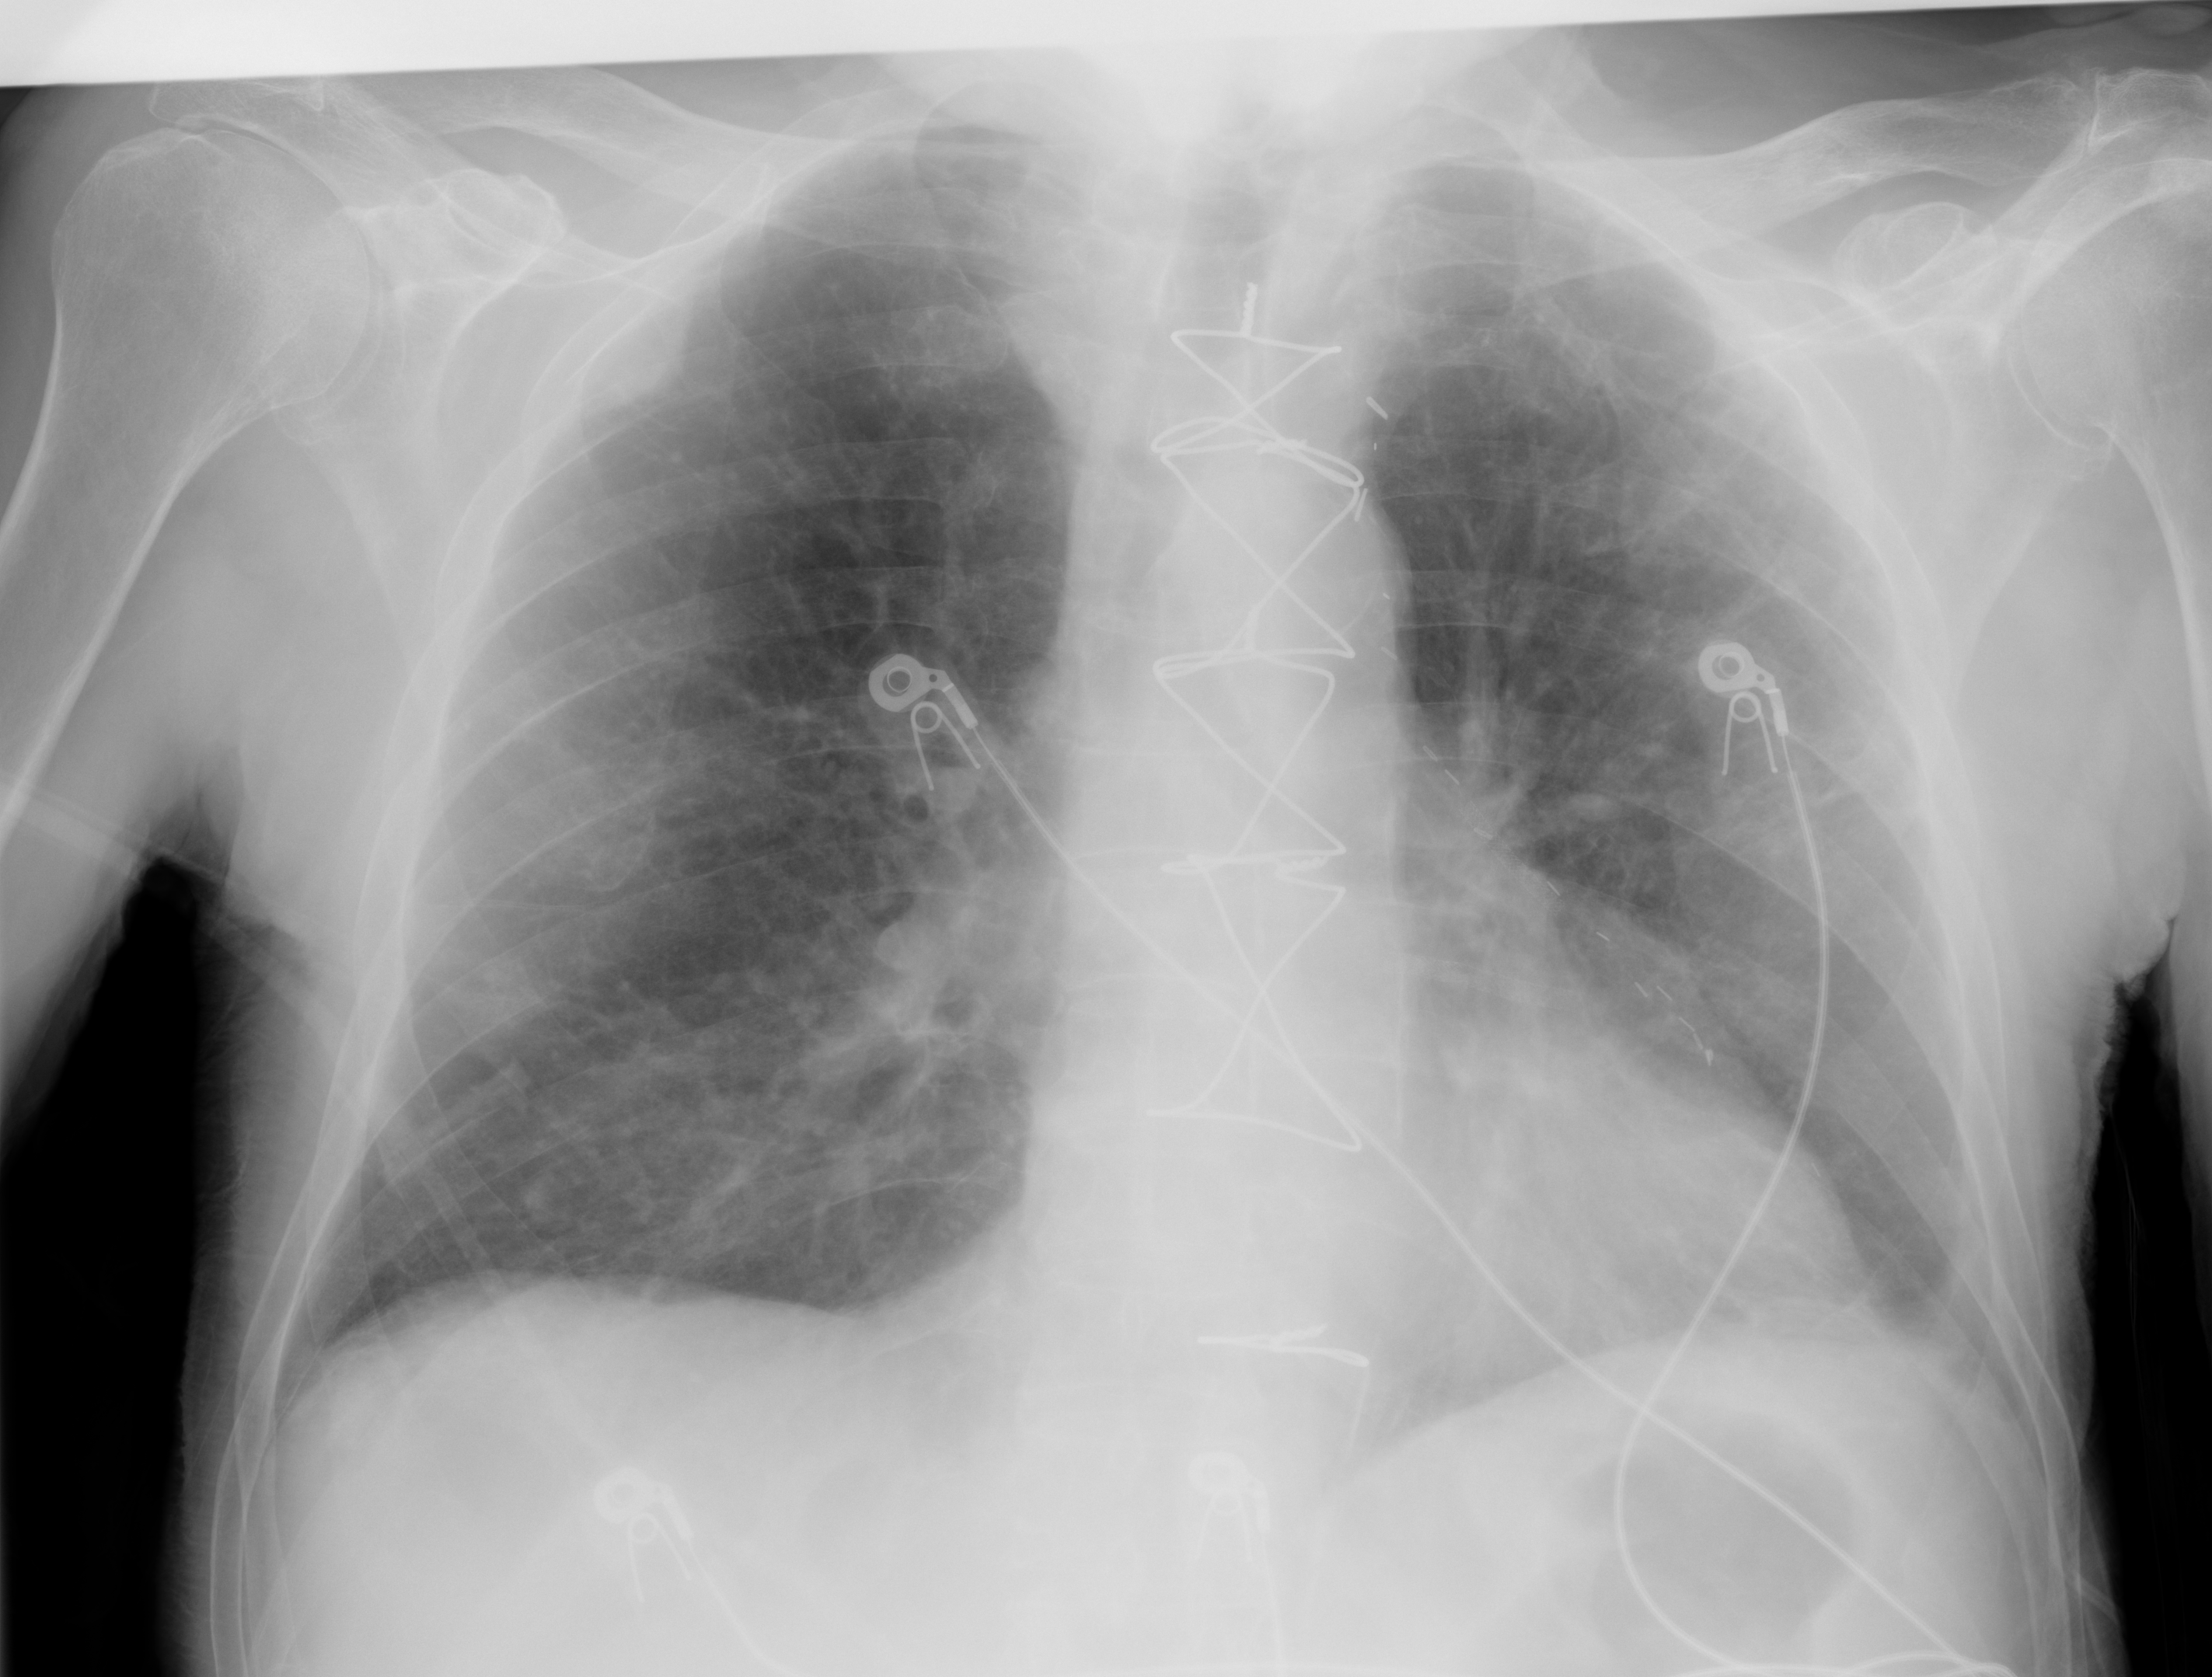
Chest X-ray (portable), AP projection. Male patient, age 81 years; imaged 1 day before the COVID-19 diagnosis.
Radiologist key findings (as recorded): The lungs are slightly hypoinflated with left basilar atelectasis. The right lung is predominantly clear.